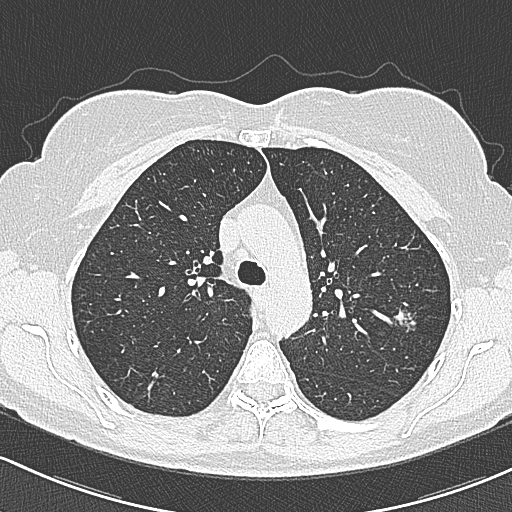
Low-dose screening chest CT, axial slice; baseline annual screen; lung window (W 1500 / L -600 HU); slice 91 of 312 in the series. Female, age 65 years at enrolment.
Lesion marked by an expert reader, bounding box <386,300,425,337> (left, top, right, bottom; pixels). The screening reader recorded 3 non-calcified nodules or masses ≥4 mm on this exam; which of them this box marks is not recorded. Official screen result: positive, change unspecified: nodule(s) >= 4 mm or enlarging nodule(s), mass(es), or other non-specific abnormalities suspicious for lung cancer. Later outcome: lung cancer diagnosed 390 days after this screen (after the second annual screen) — bronchiolo-alveolar carcinoma, non-mucinous, left upper lobe, stage IA (AJCC 6th edition), 10 mm at pathology.